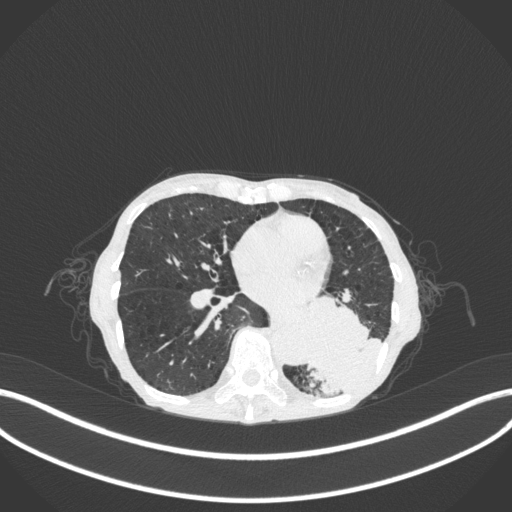
Chest CT, one axial slice. Reconstruction kernel B31f. Lung window (W 1500 / L -600 HU). 1 mm slice thickness. 512 × 512 image matrix, field of view 400 × 400 mm. Female patient, age 70 years. Case-level facts recorded for this patient, not image findings: clinical TNM (as recorded): T3 N0 M0.
Outlined on this slice (rectangle marked by the reading radiologist):
- lung tumour (recorded histology: small cell carcinoma): bounding box [x1, y1, x2, y2] px = [297, 292, 383, 397]